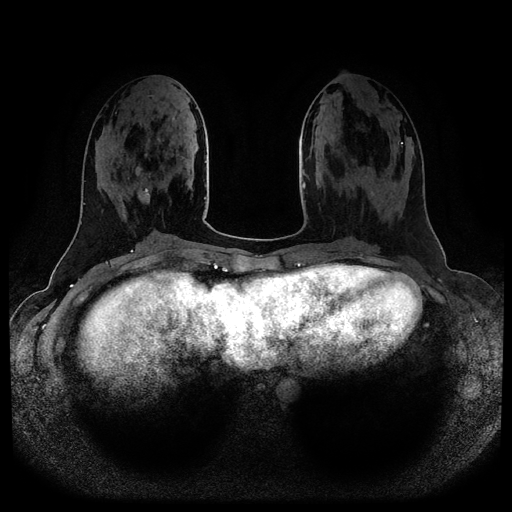
Breast MRI (dynamic contrast-enhanced, multi-phase), one axial slice; slice 38 of 116 in the series (ordered by position); dynamic contrast-enhanced series, time point 2 of 5 at this slice position (early post-contrast); 1.5 T; TE 2.6 ms, TR 5.2 ms; 2 mm slice thickness; 512 × 512 image matrix, field of view 380 × 380 mm. Female patient, age 25 years.
Structures marked on this image (semi-automatic segmentation, software-assisted and operator-edited):
- breast lesion (labelled benign in the annotation): box from (x=137, y=186) to (x=151, y=204) px